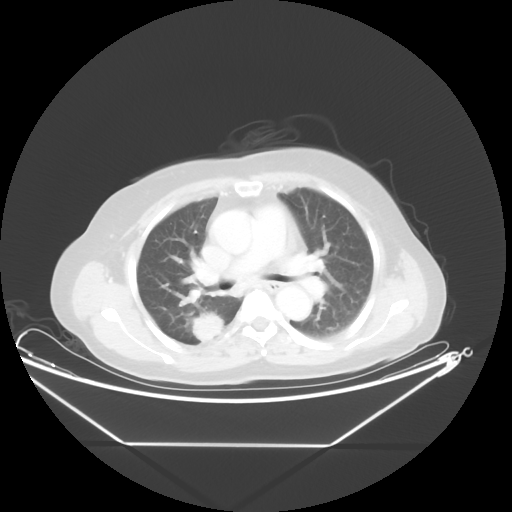
Chest CT, one axial slice. Position 29 of 48 along the scan axis. Reconstruction kernel STANDARD. 100 kVp. Lung window (W 1500 / L -600 HU). 5 mm slice thickness. 512 × 512 image matrix, field of view 462 × 462 mm. Patient: female, 62 years. Case-level facts recorded for this patient, not image findings: clinical TNM (as recorded): T1c N0 M0; histopathological grade: G2-3.
Annotated regions visible in this slice (bounding box drawn by a radiologist):
- lung tumour (recorded histology: adenocarcinoma): bounding box <178,300,231,347> (left, top, right, bottom; pixels)